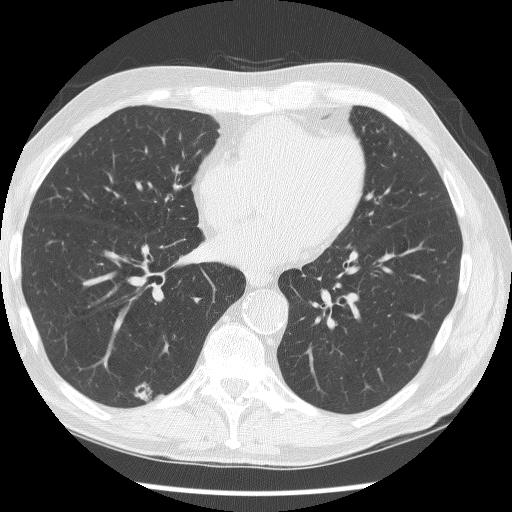
Low-dose screening chest CT, axial slice; baseline annual screen; lung window (W 1500 / L -600 HU); 2.5 mm slice thickness; lung (sharp) reconstruction kernel (BONE); 120 kVp; slice 105 of 190 in the series. Male participant, aged 62 years at enrolment. Current smoker at enrolment.
- Lesion marked by an expert reader, box from (x=125, y=379) to (x=164, y=411) px.
- The screening reader recorded 2 non-calcified nodules or masses ≥4 mm on this exam (right lower lobe, right lower lobe); which of them this box marks is not recorded.
- Lung cancer was diagnosed 849 days after this screen: adenocarcinoma, NOS, right lower lobe, moderately differentiated (G2), stage IIIB (AJCC 6th edition), 15 mm at pathology.